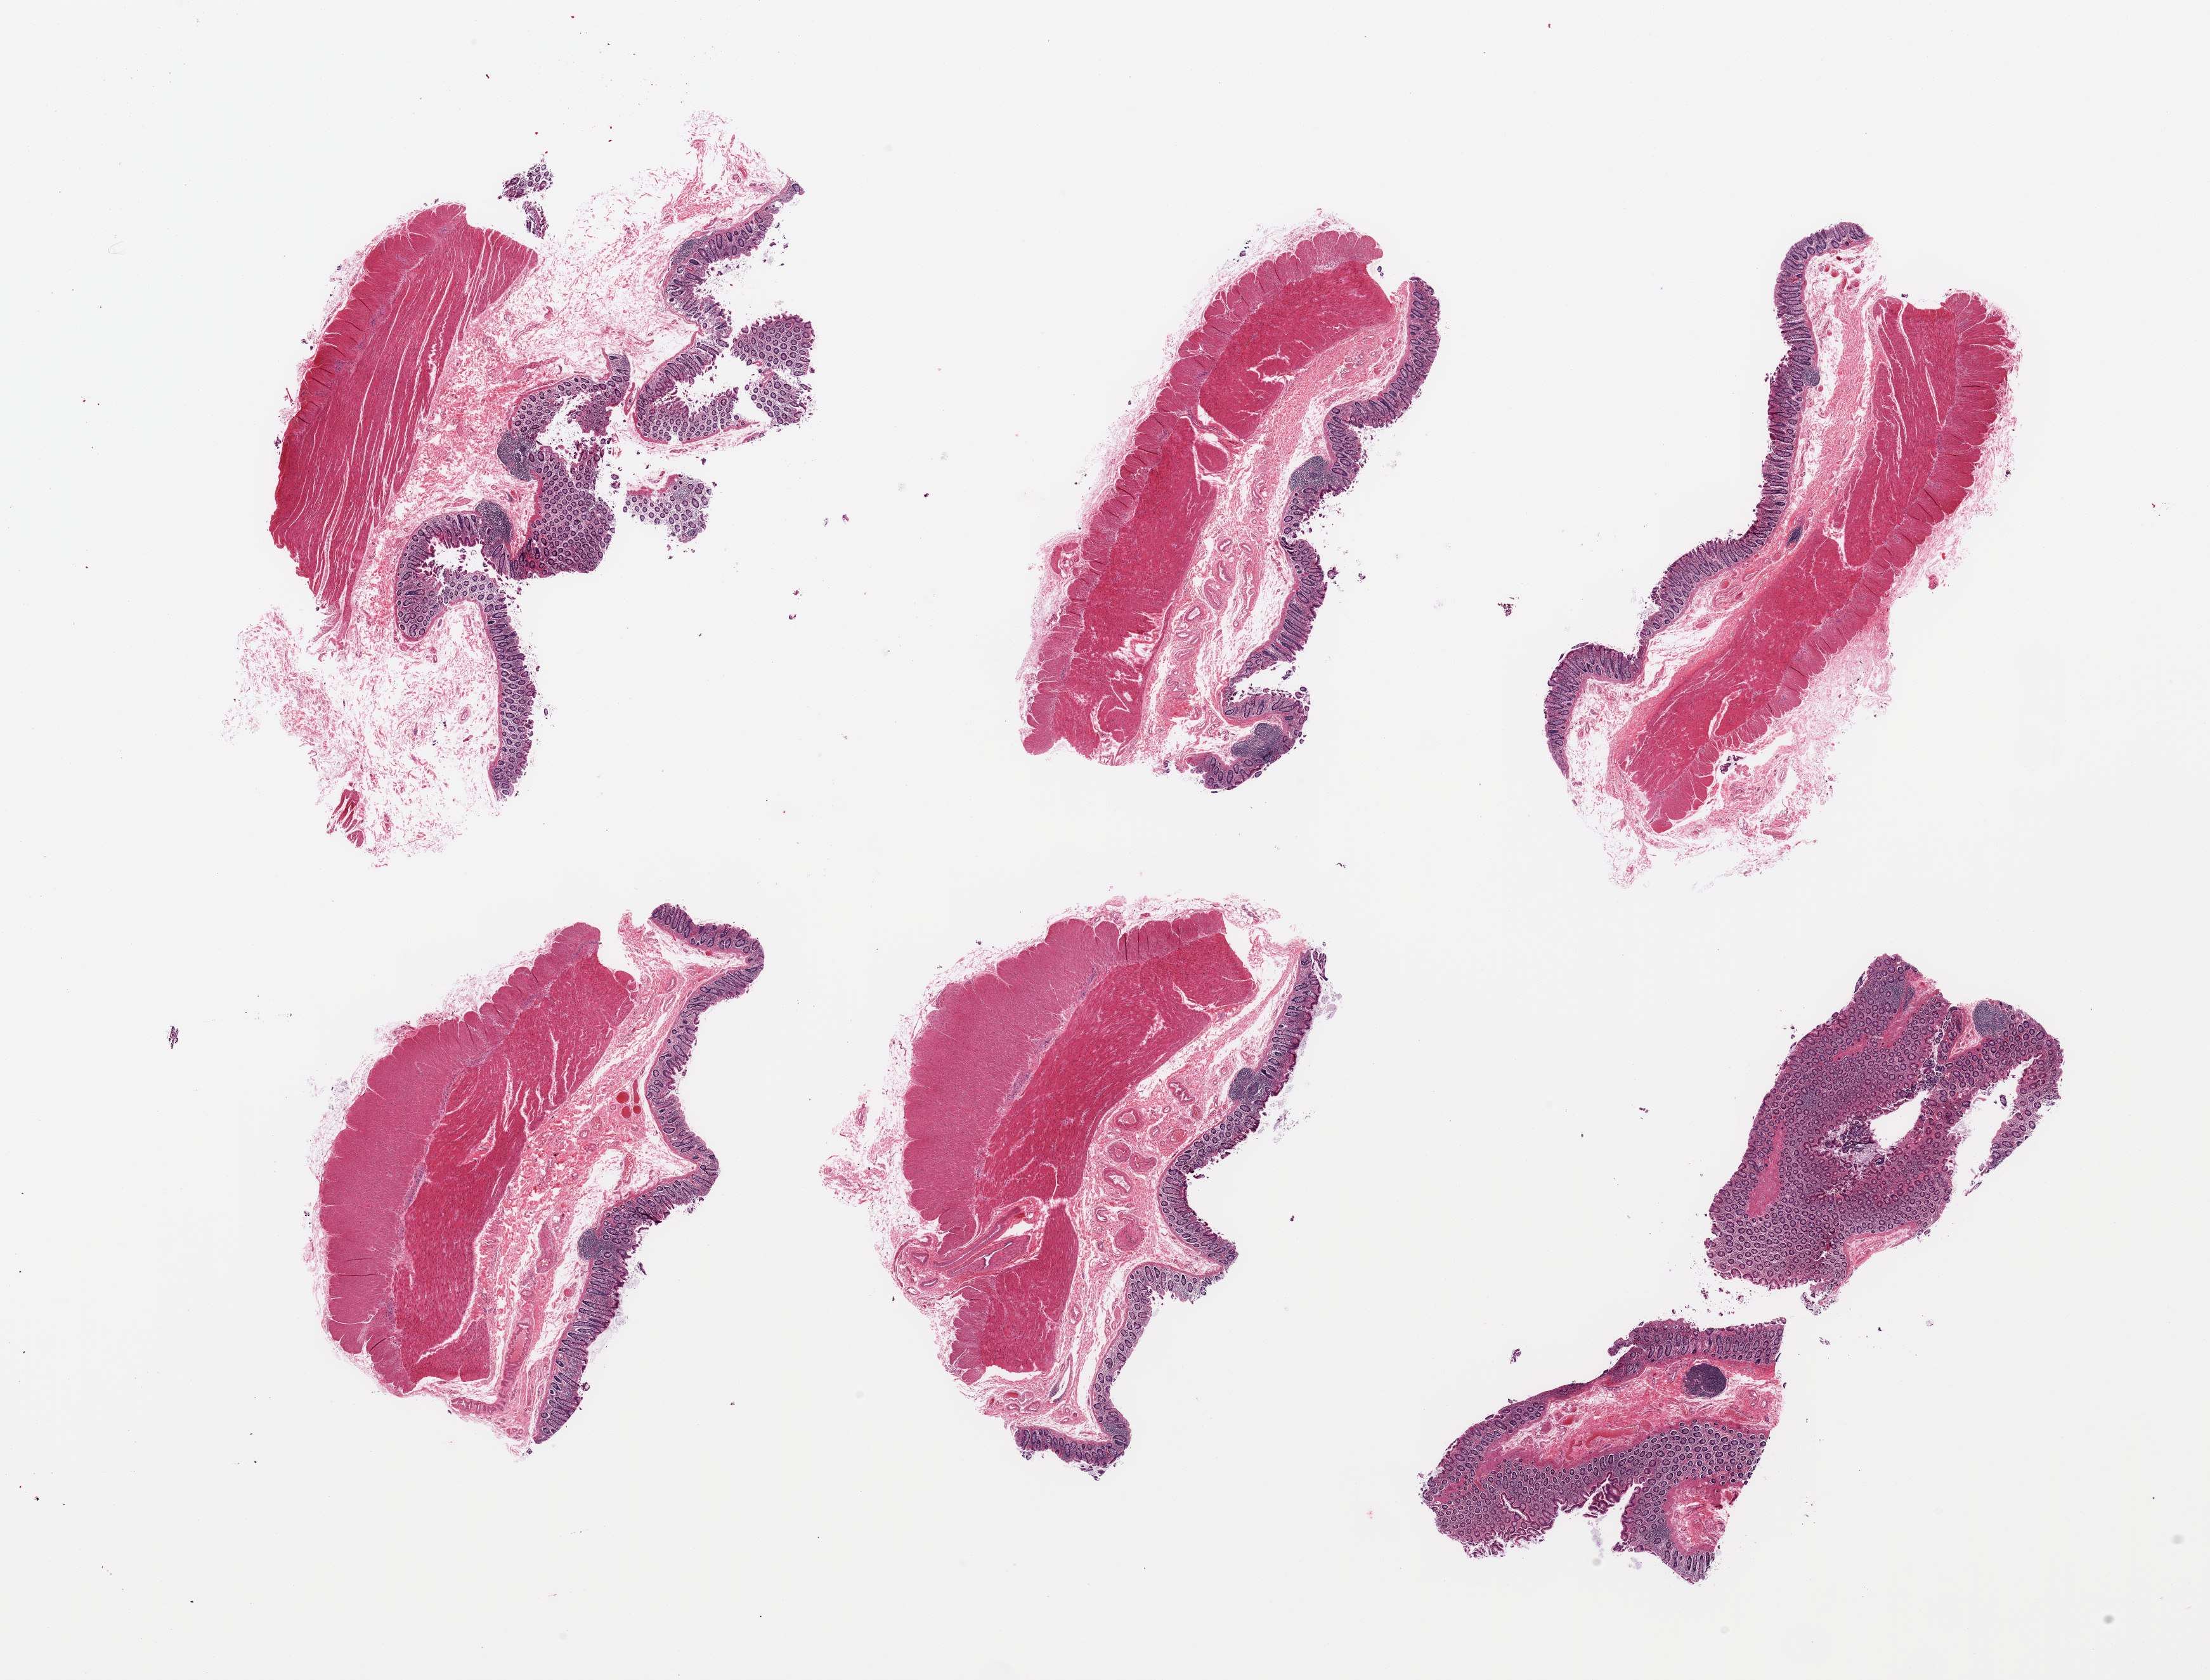
Whole-slide image, haematoxylin and eosin stain, brightfield — a low-resolution overview of the entire scanned area, about 27.6 x 21.0 mm. PAXgene-fixed, paraffin-embedded tissue. Sampled site (target tissue): transverse colon. Donor tissue sample. Donor: female.
* review note (as recorded): 6 pieces, target mucosa up to ~0.4mm, ~15% thickness